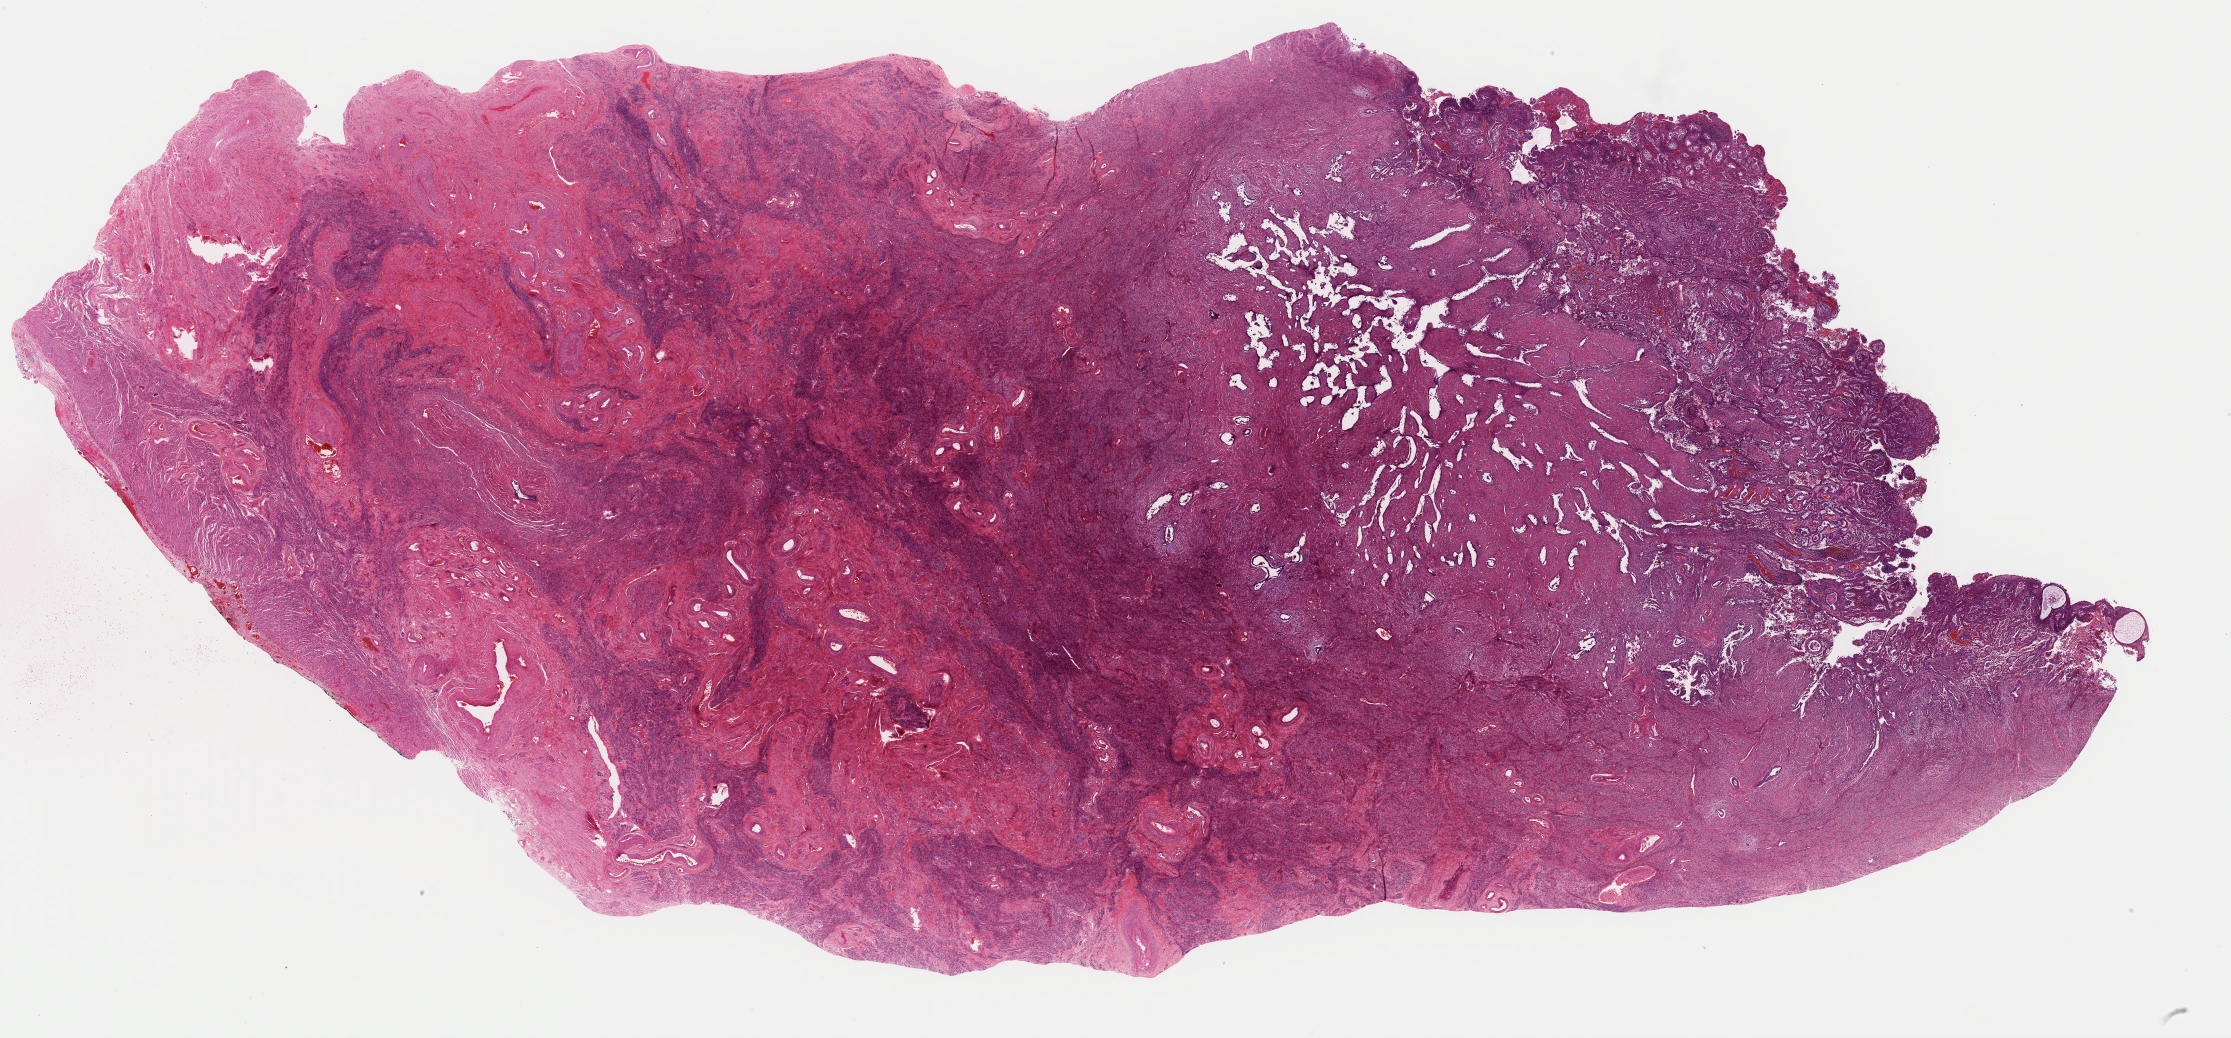
Digitized H&E-stained tissue section (whole slide) — shown as a low-resolution overview of the whole scanned area (about 35.2 x 16.4 mm, slide scanned at 40x). Formalin-fixed paraffin-embedded (FFPE) diagnostic section. Primary tumour sample from the uterus. Female, age 69 years at initial diagnosis. Histologic grade: G3 (poorly differentiated).
• diagnosis: Serous cystadenocarcinoma, NOS
• FIGO stage: IIIA